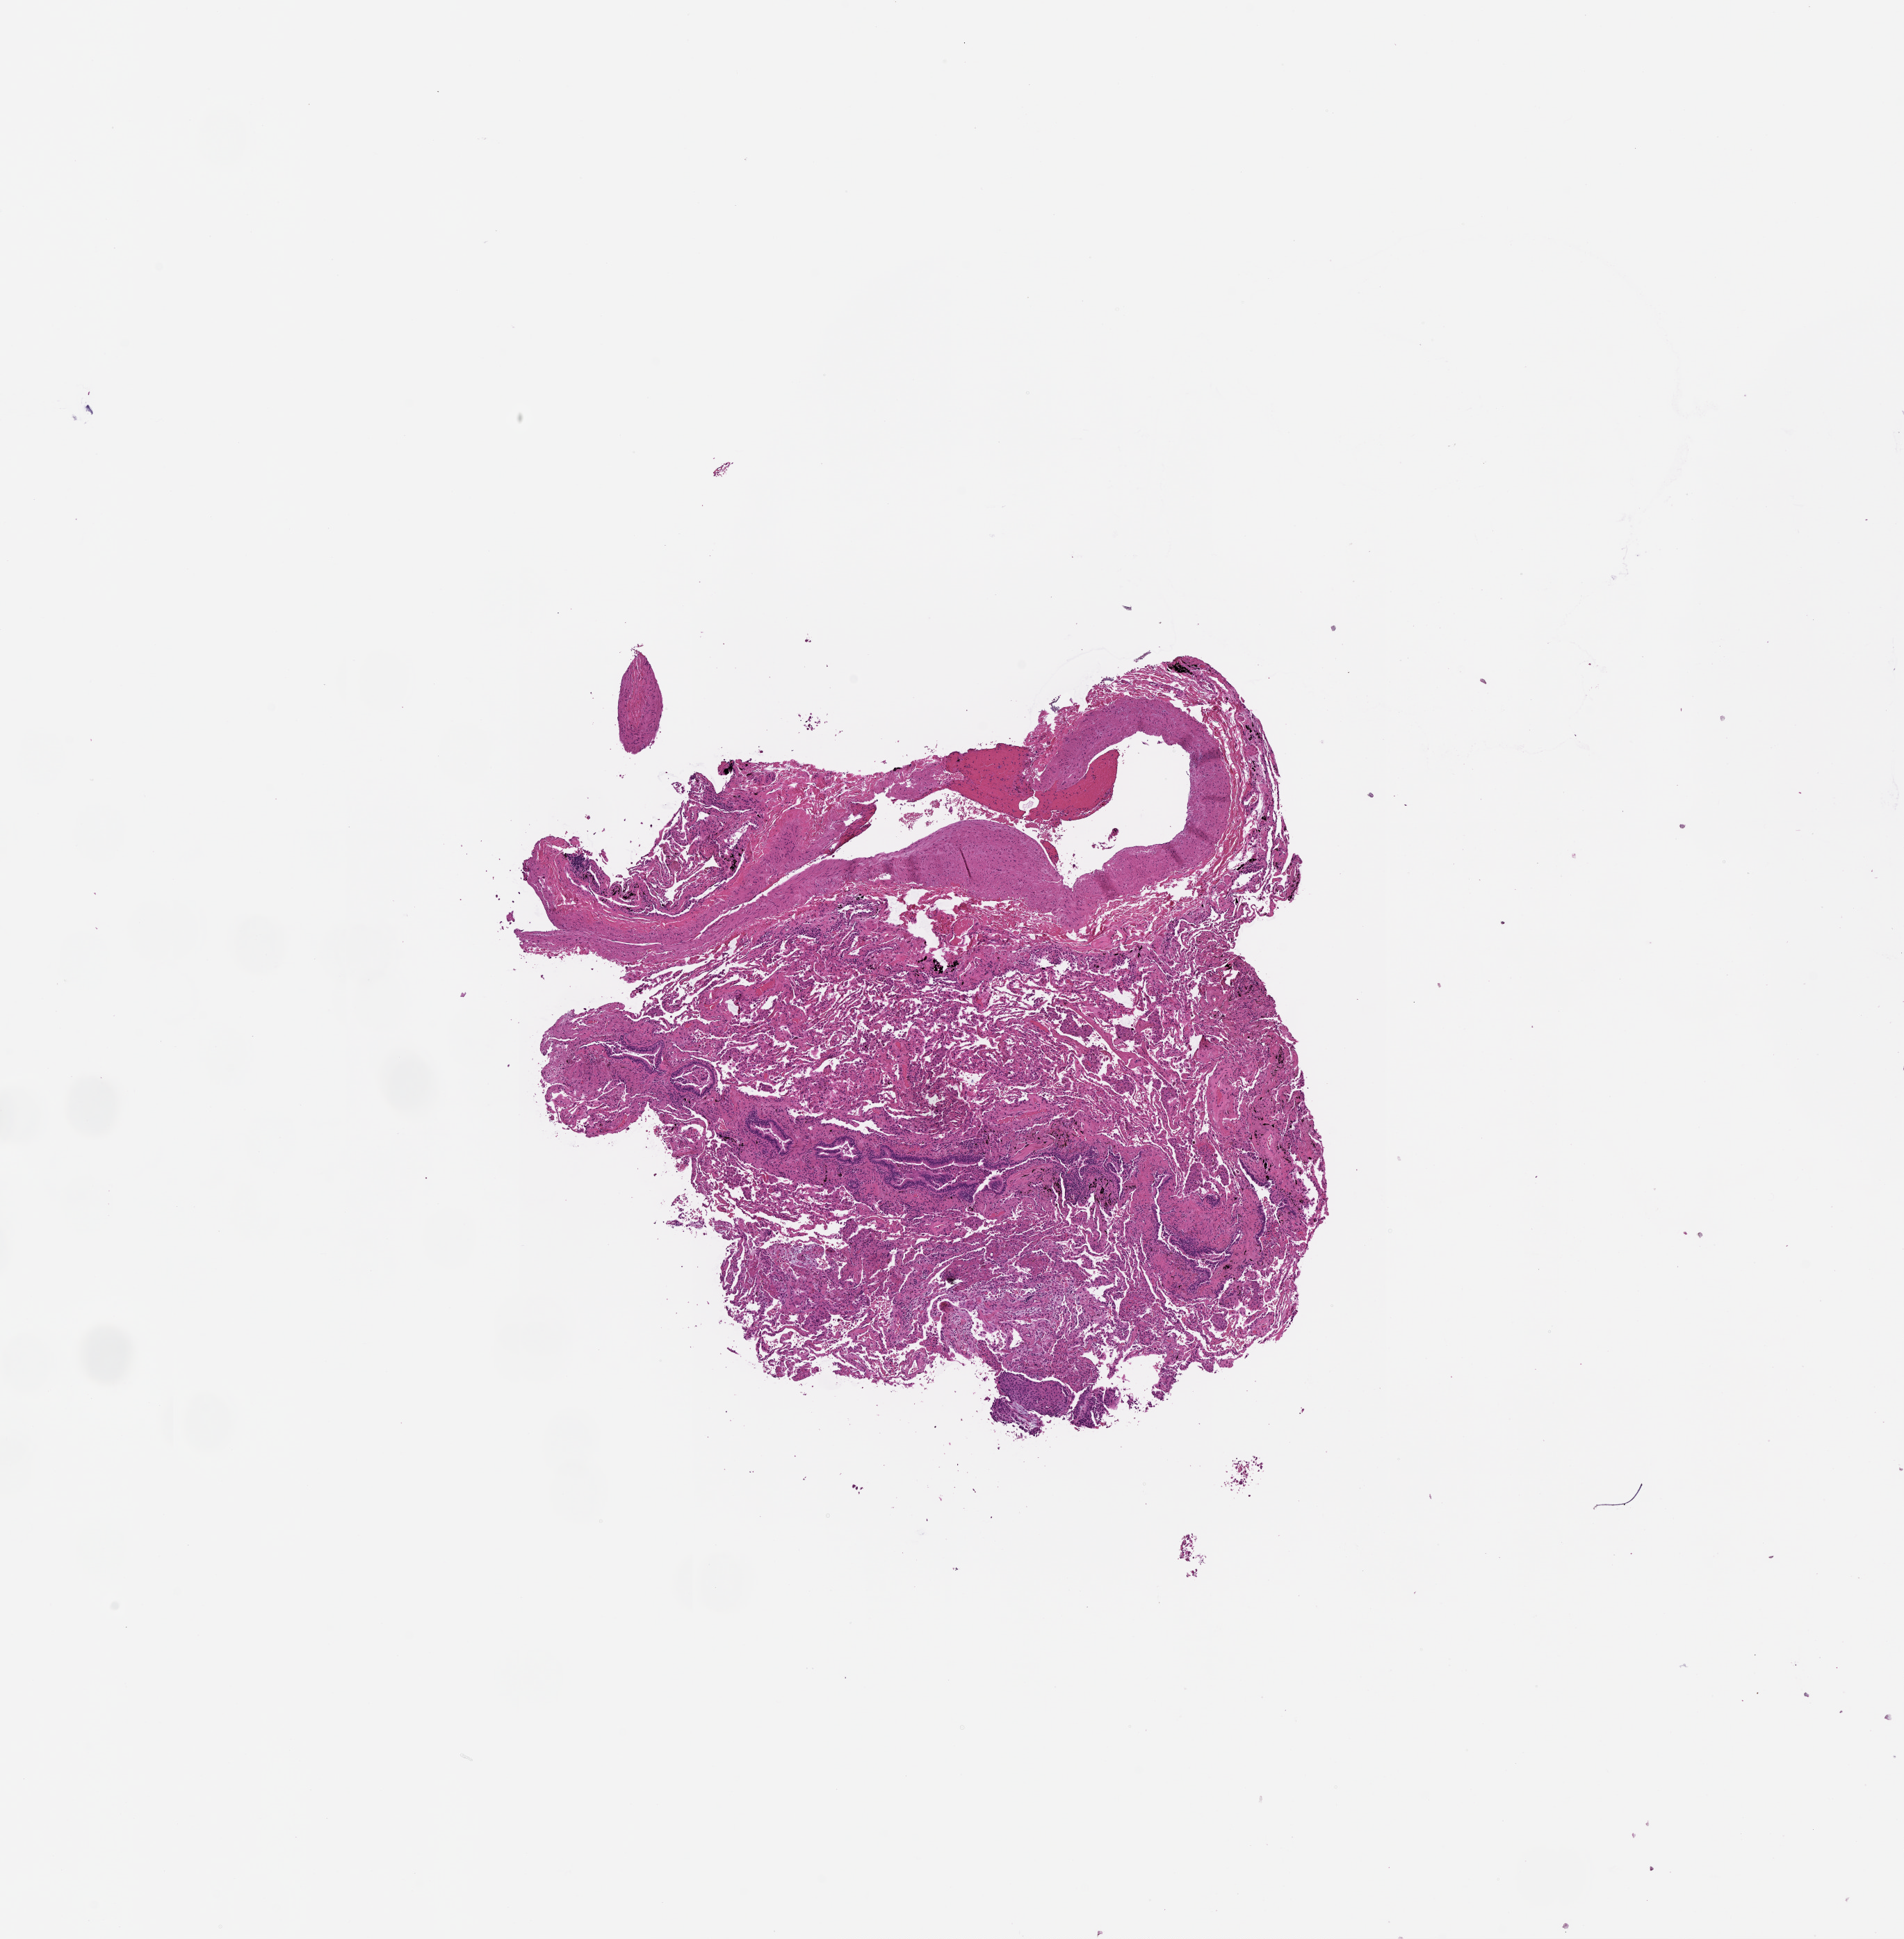
H&E whole-slide image — whole scanned area (about 11.0 x 11.2 mm) shown as a low-resolution overview, lung, tissue type not recorded.
Patient diagnosis (cohort enrolment): squamous cell carcinoma (lung).